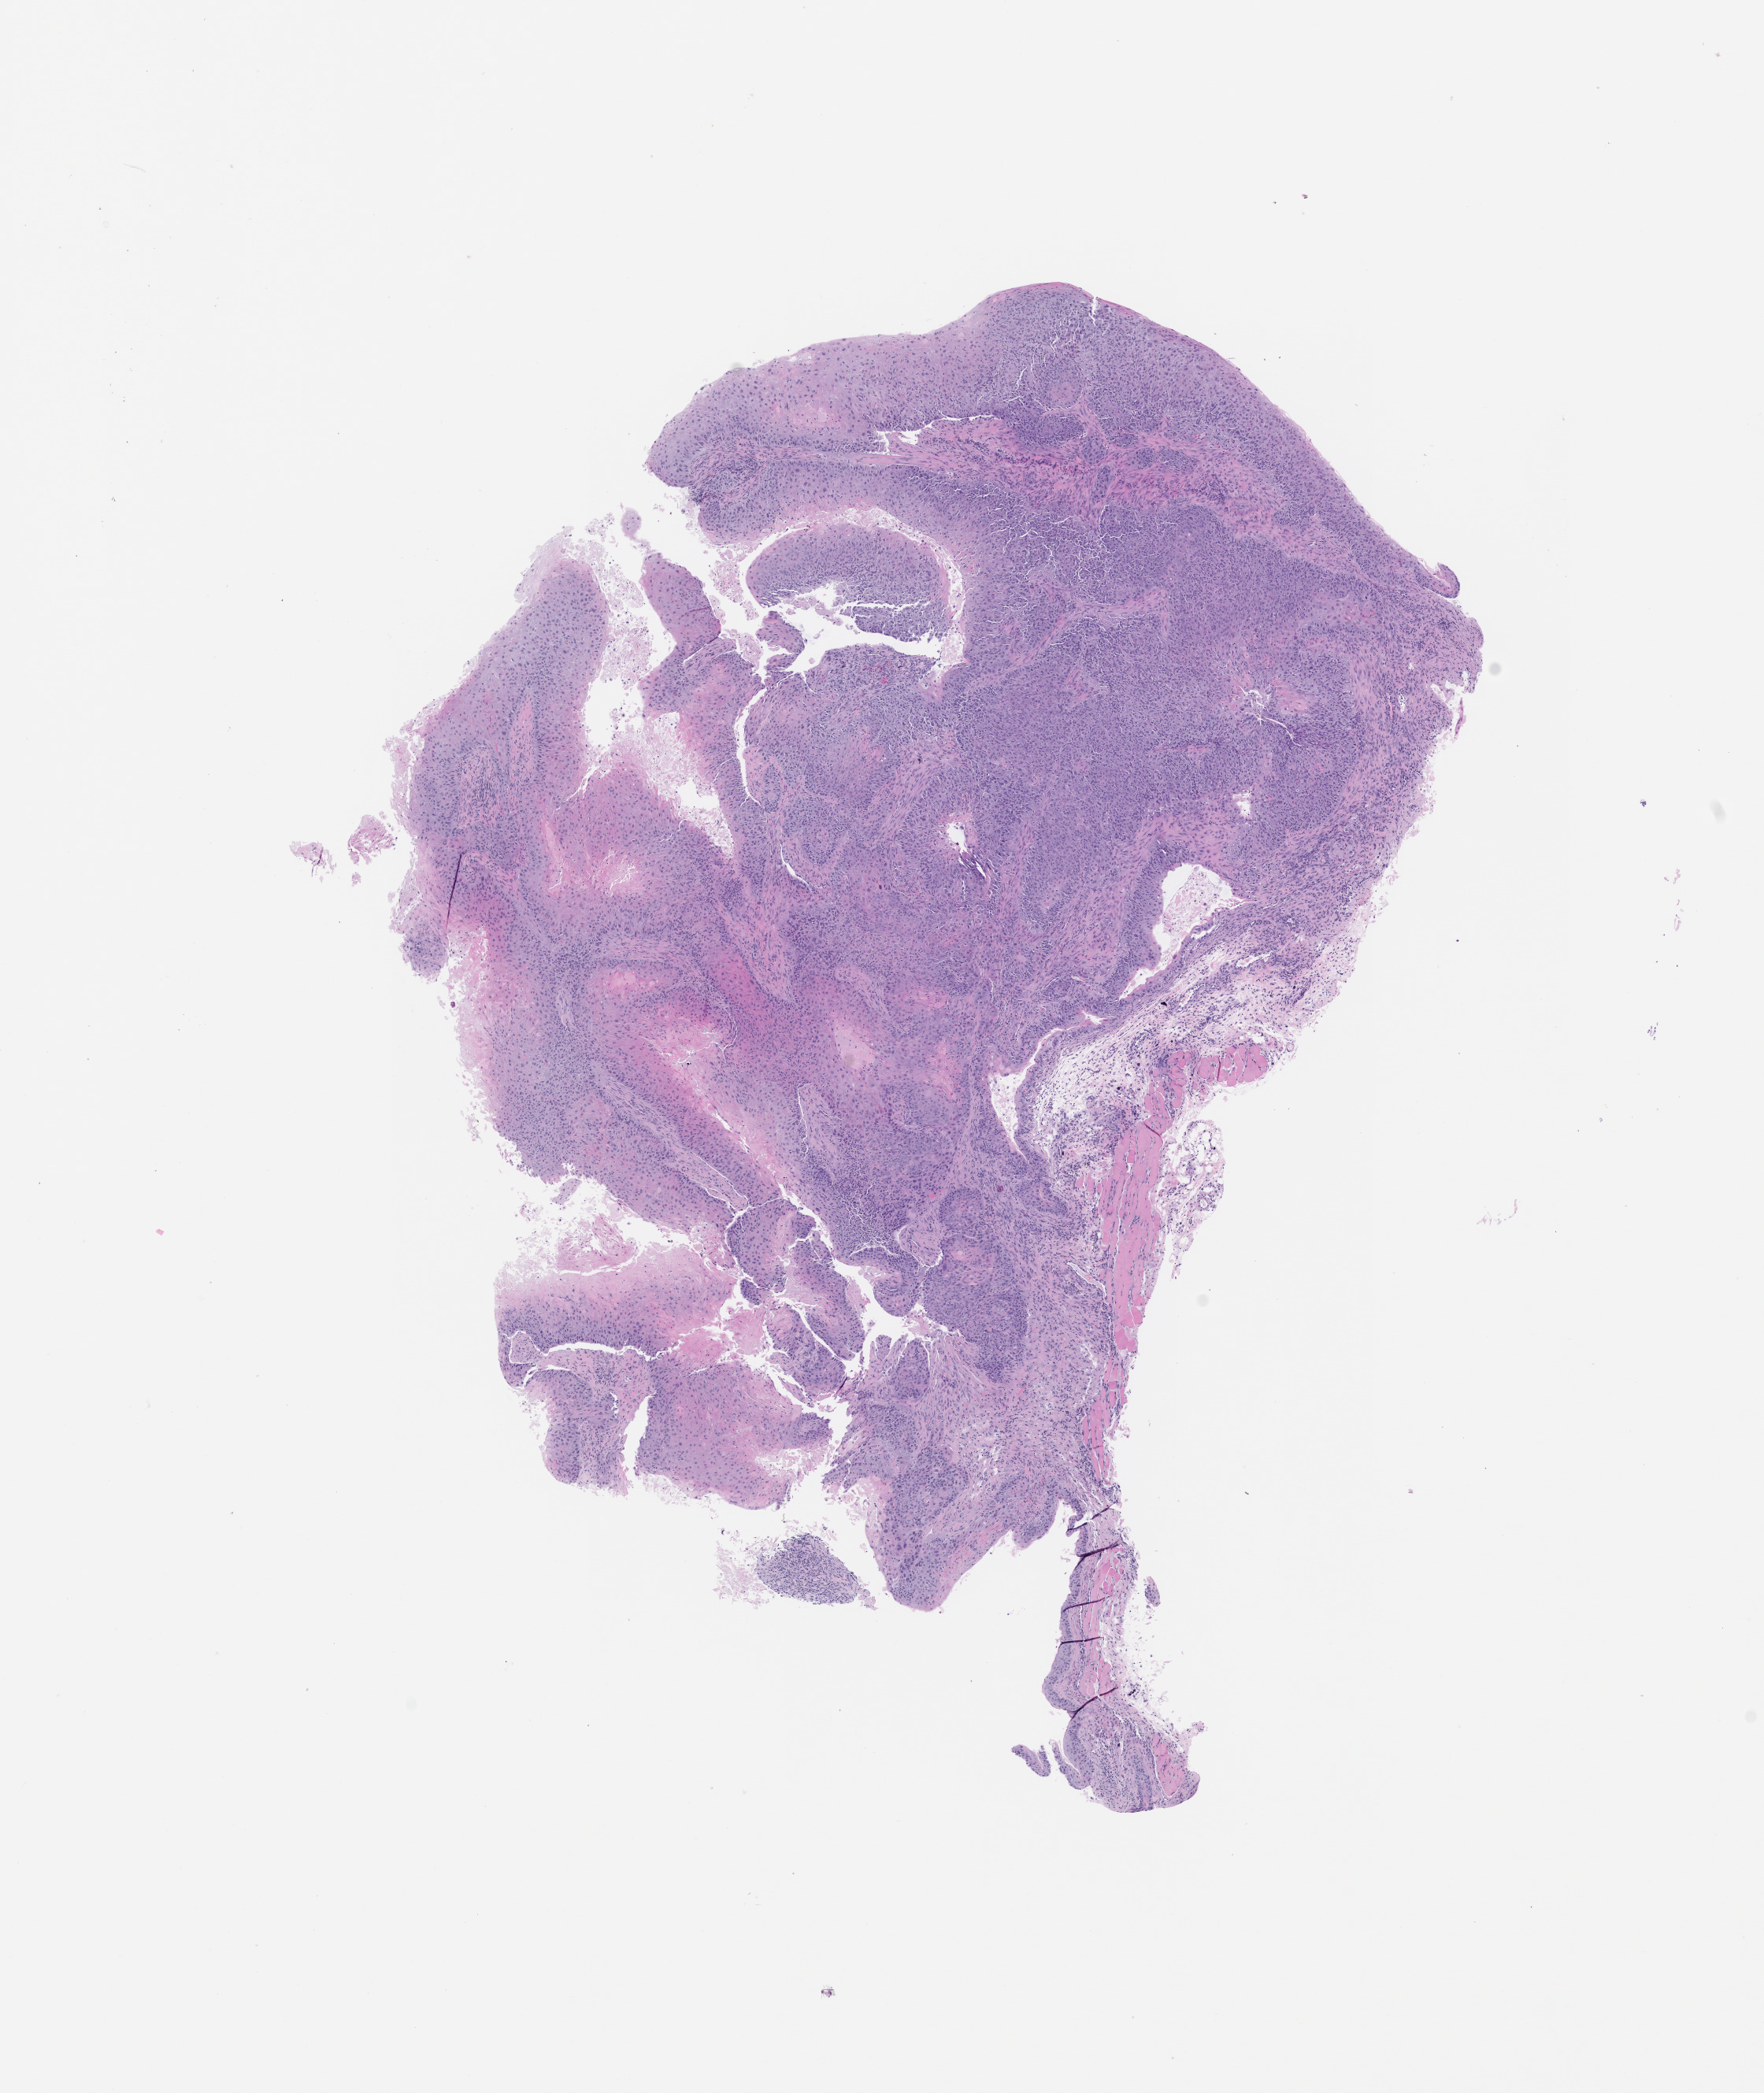
Haematoxylin and eosin whole-slide image of a patient-derived xenograft (PDX) tumor grown in a mouse, passage 1 — shown as a low-resolution overview of the whole scanned area (about 9.0 x 10.6 mm). FFPE section. Tumor site category: lung.
Originating patient diagnosis: Lung Squamous Cell Carcinoma.